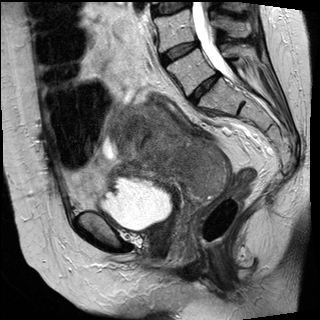
Pelvic MRI for cervical cancer, one sagittal slice. T2-weighted. 1.5 T. TE 89 ms, TR 3810 ms. 320 × 320 image matrix, field of view 260 × 260 mm. Patient: female, 62 years.
Structures marked on this image (outlined manually by an expert reader):
- uterus and cervix: bounding box [x1, y1, x2, y2] px = [109, 101, 231, 201]